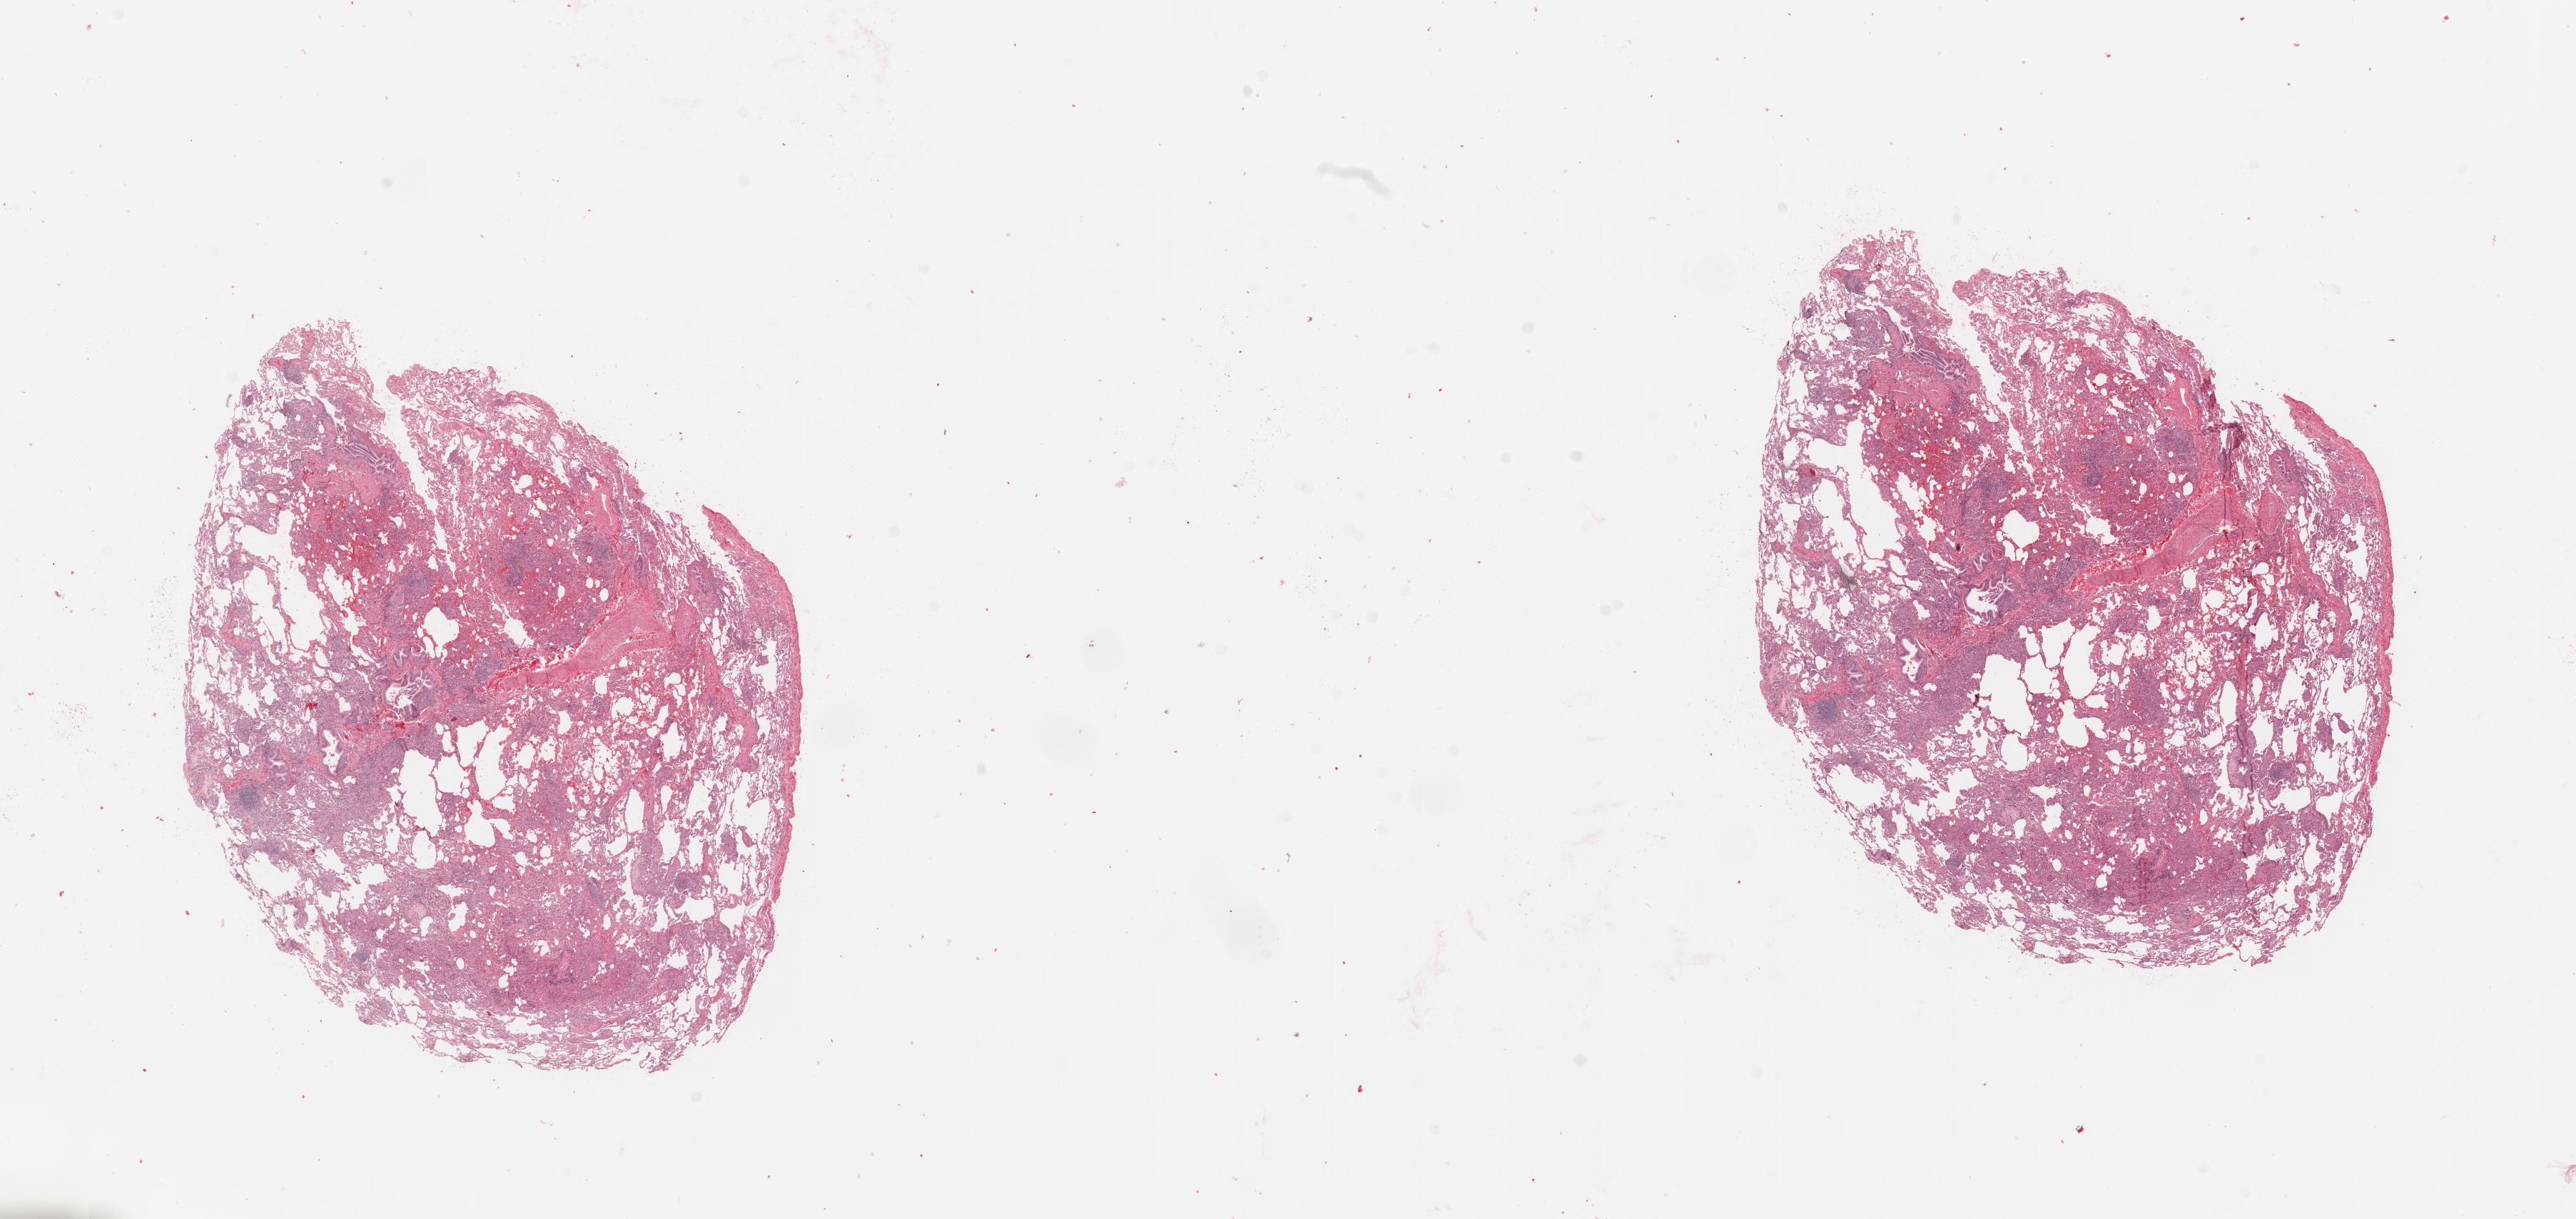
H&E whole-slide image, shown as a low-resolution overview of the whole scanned area (about 28.5 x 13.5 mm). Lung, normal (non-tumour) tissue. Patient: female, age 77 years.
This section: normal (non-tumour) tissue from the same patient. Patient diagnosis: Squamous cell carcinoma, NOS.